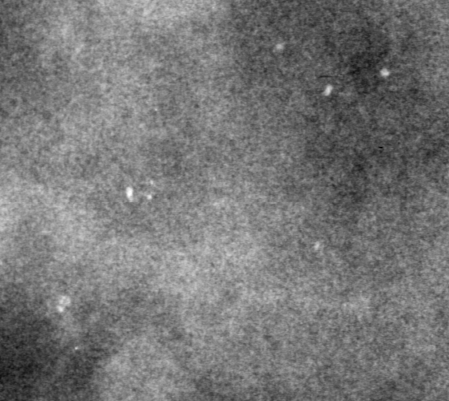
Cropped region of a digitized screen-film mammogram centred on a radiologist-marked abnormality, right breast, CC view.
Finding: calcifications, morphology pleomorphic, distribution segmental; BI-RADS assessment category 4; pathology (as recorded): benign.